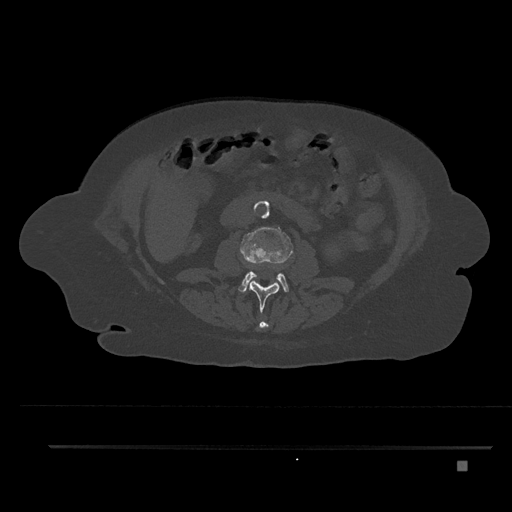
CT including the spine, one axial slice; slice 157 of 797 in the series (ordered by position); reconstruction kernel Br40s/3; bone window (W 1800 / L 400 HU); 0.5 mm slice thickness; 512 × 512 image matrix, field of view 437 × 437 mm. Female patient, age 76 years. From the clinical record (not read from this slice): primary cancer: lung; vertebrae with lytic lesions (as recorded): T11, L3.
Structures marked on this image (semi-automatic segmentation, software-assisted and operator-edited):
- L1 vertebra: bounding box (x1, y1, x2, y2) in pixels: (258, 321, 269, 330)
- L2 vertebra: (248, 265, 279, 313)
- L3 vertebra: (239, 227, 293, 293)